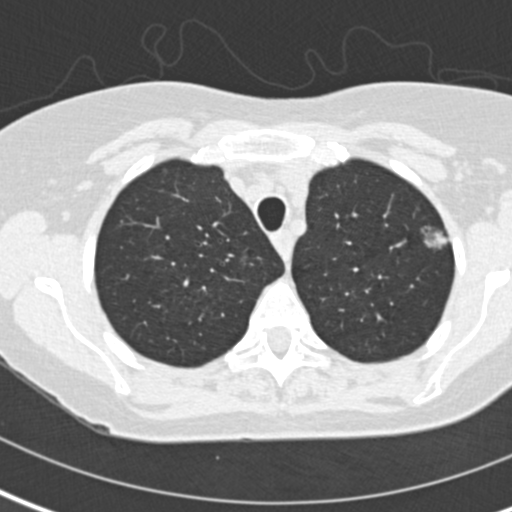
Low-dose screening chest CT, one axial slice. Position 115 of 141 along the scan axis. Lung window (W 1500 / L -600 HU). 2 mm slice thickness. 512 × 512 image matrix.
Annotated regions visible in this slice (outlined manually by an expert reader):
- lesion 1 (tumor, upper lobe of left lung): box from (x=421, y=226) to (x=450, y=248) px